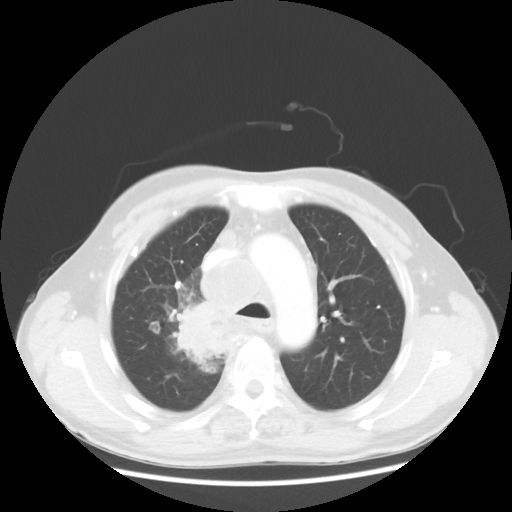
Chest CT, one axial slice. Reconstruction kernel STANDARD. Lung window (W 1500 / L -600 HU). 512 × 512 image matrix, field of view 382 × 382 mm. Male patient, age 64 years. Case-level facts recorded for this patient, not image findings: clinical TNM (as recorded): T3 N3 M0; histopathological grade: G3.
Outlined on this slice (rectangle marked by the reading radiologist):
- lung tumour (recorded histology: small cell carcinoma): bounding box (x1, y1, x2, y2) in pixels: (167, 289, 227, 368)